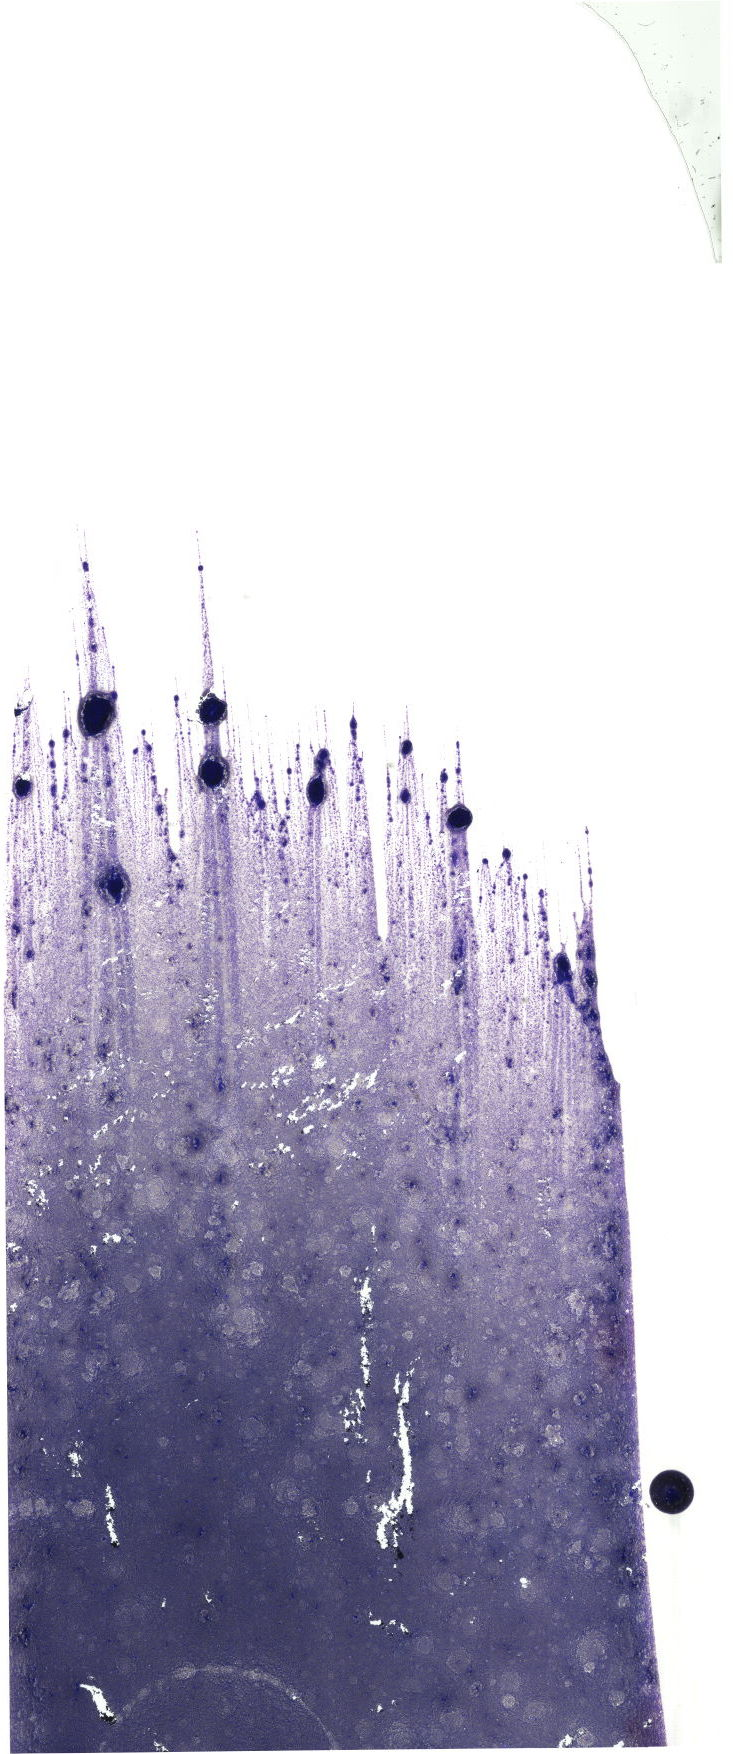
May-Grünwald-Giemsa (MGG)-stained marrow aspirate smear (whole slide) — a low-resolution overview of the entire scanned area, about 20.8 x 49.7 mm. Male patient.
Diagnosis: Chronic Phase Chronic Myeloid Leukemia, BCR-ABL1 Positive.